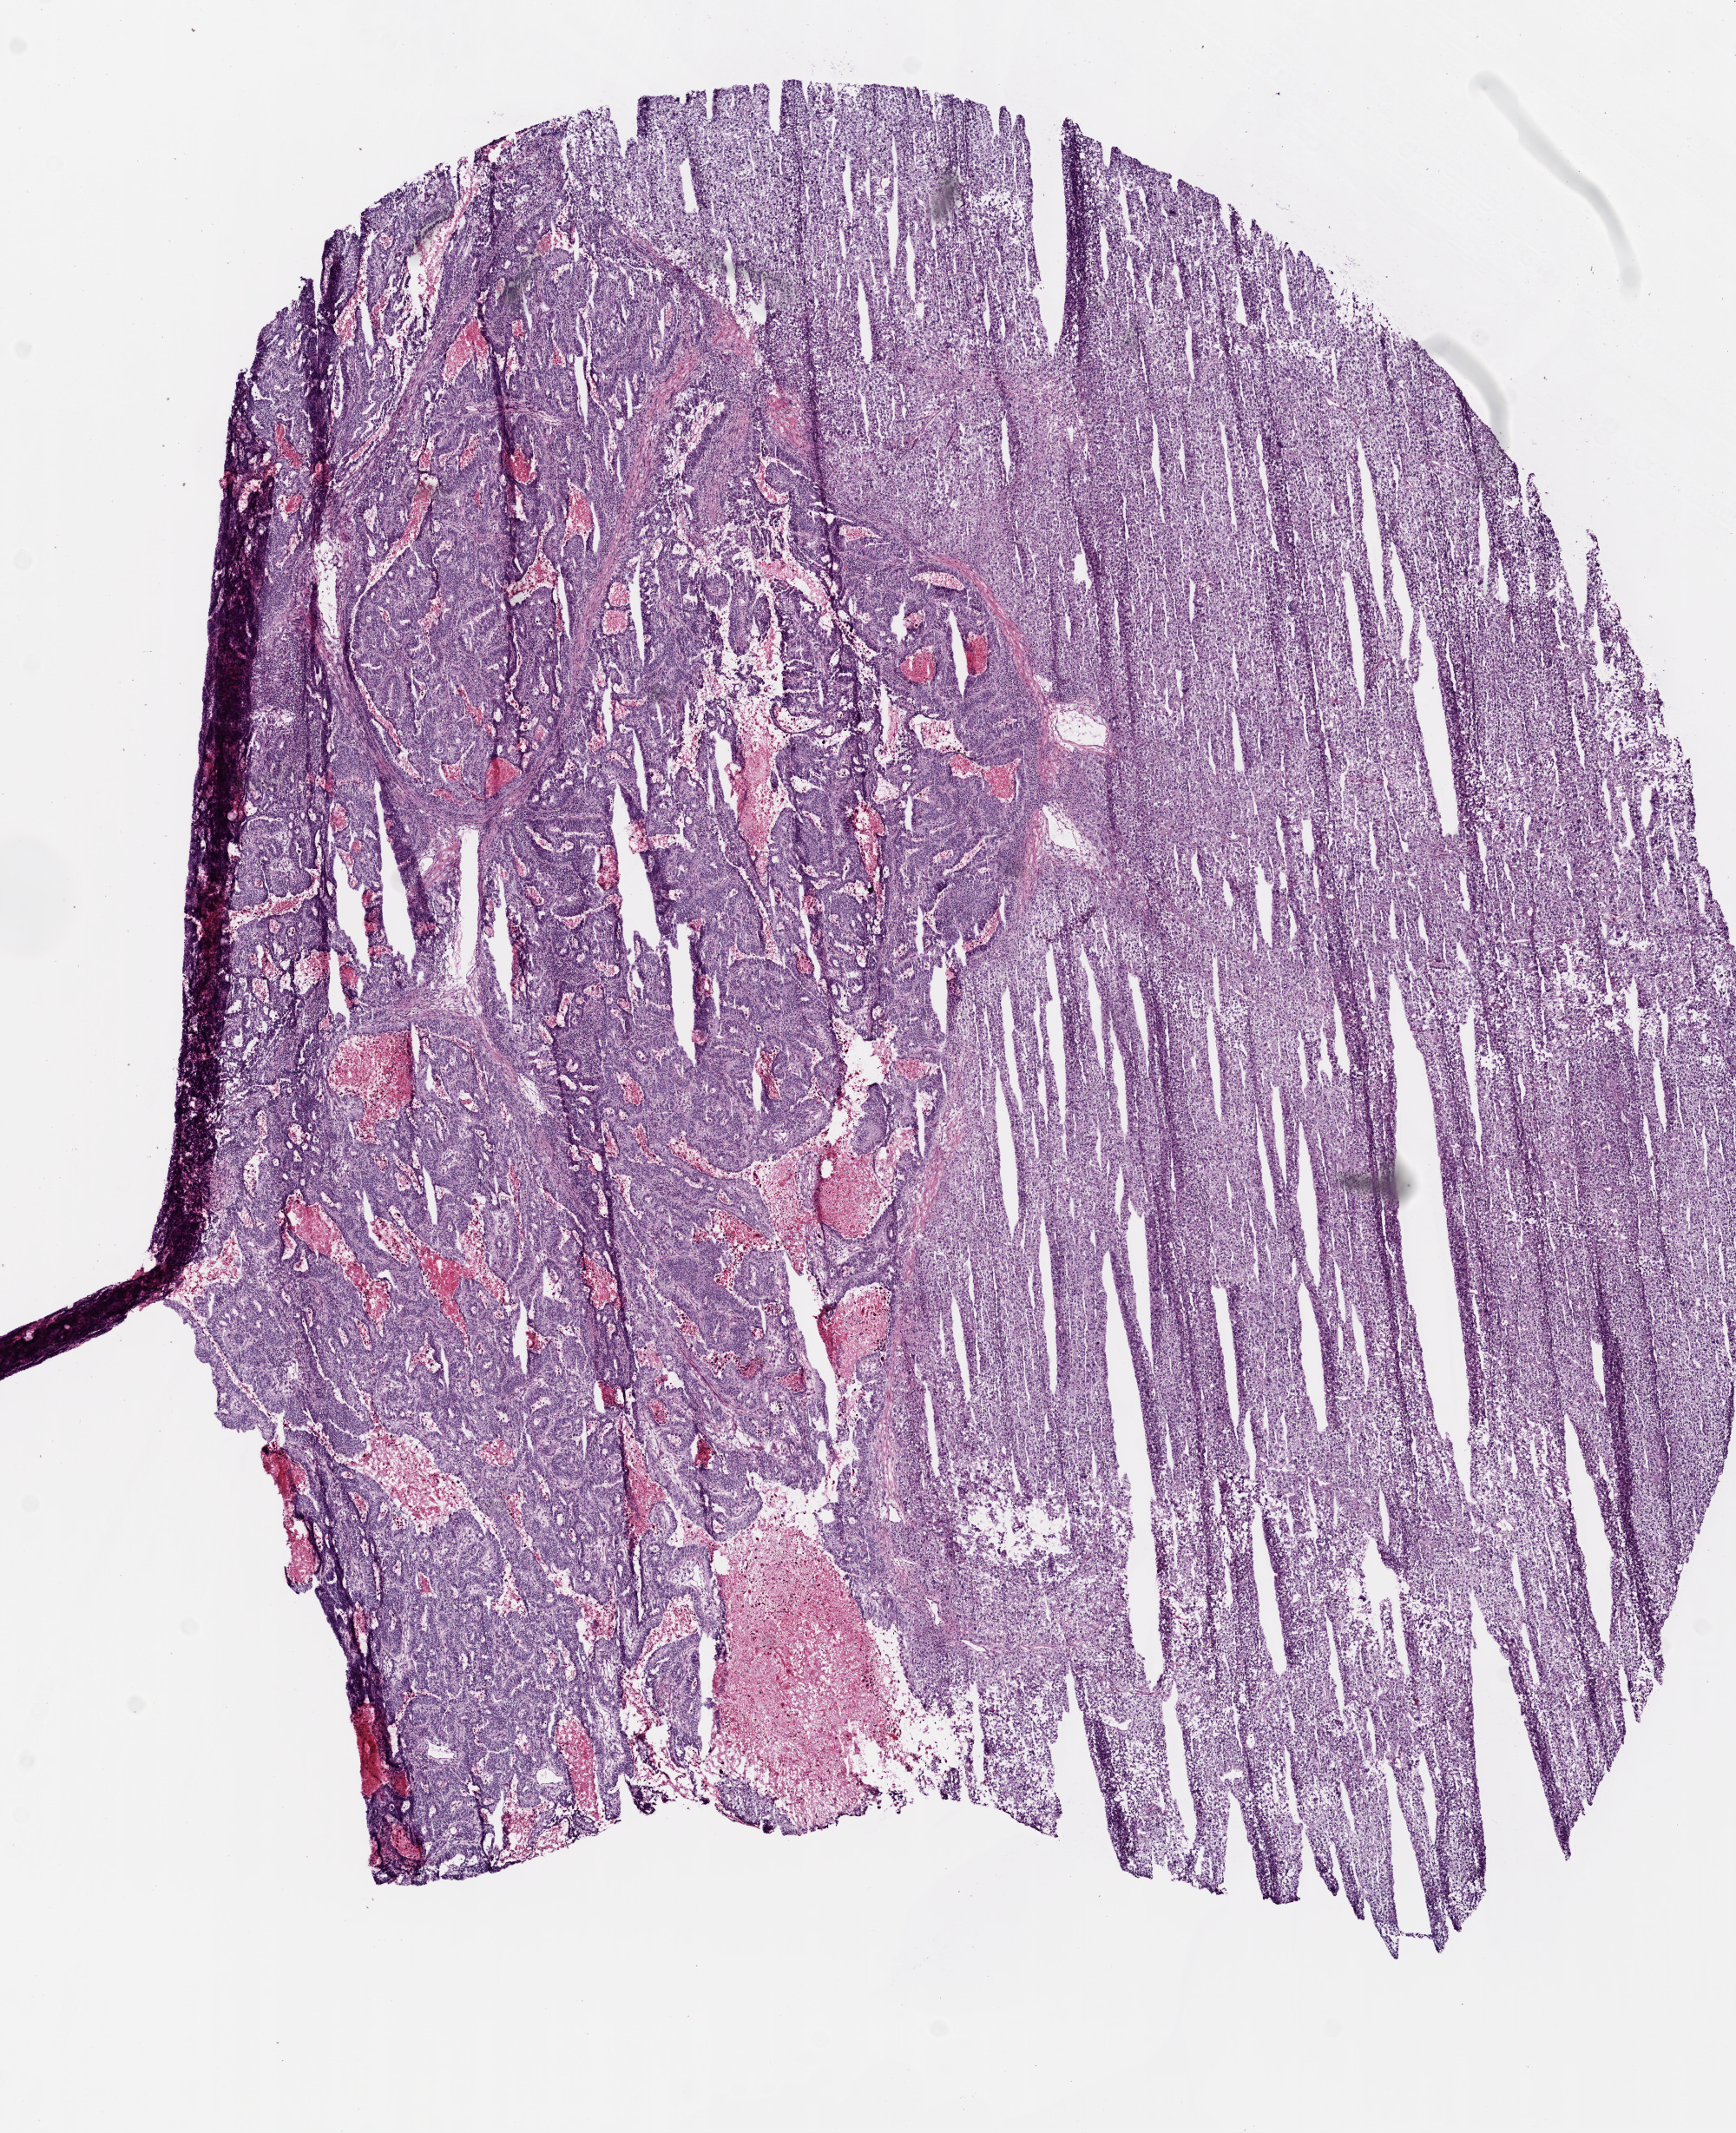
Whole-slide histology image, Hematoxylin and eosin (H&E) stained, whole scanned area (about 8.0 x 9.9 mm, acquisition: 20x scan) shown as a low-resolution overview; frozen section from the bottom of the tissue portion; primary tumour sample from the lung. Male, age 65 years at initial diagnosis. Pathologist review of this section (percent, as recorded): tumour nuclei 75%, normal cells 0%, stromal cells 5%, necrosis 10%.
* pathologic diagnosis: Adenocarcinoma with mixed subtypes
* AJCC pathologic stage: IIB